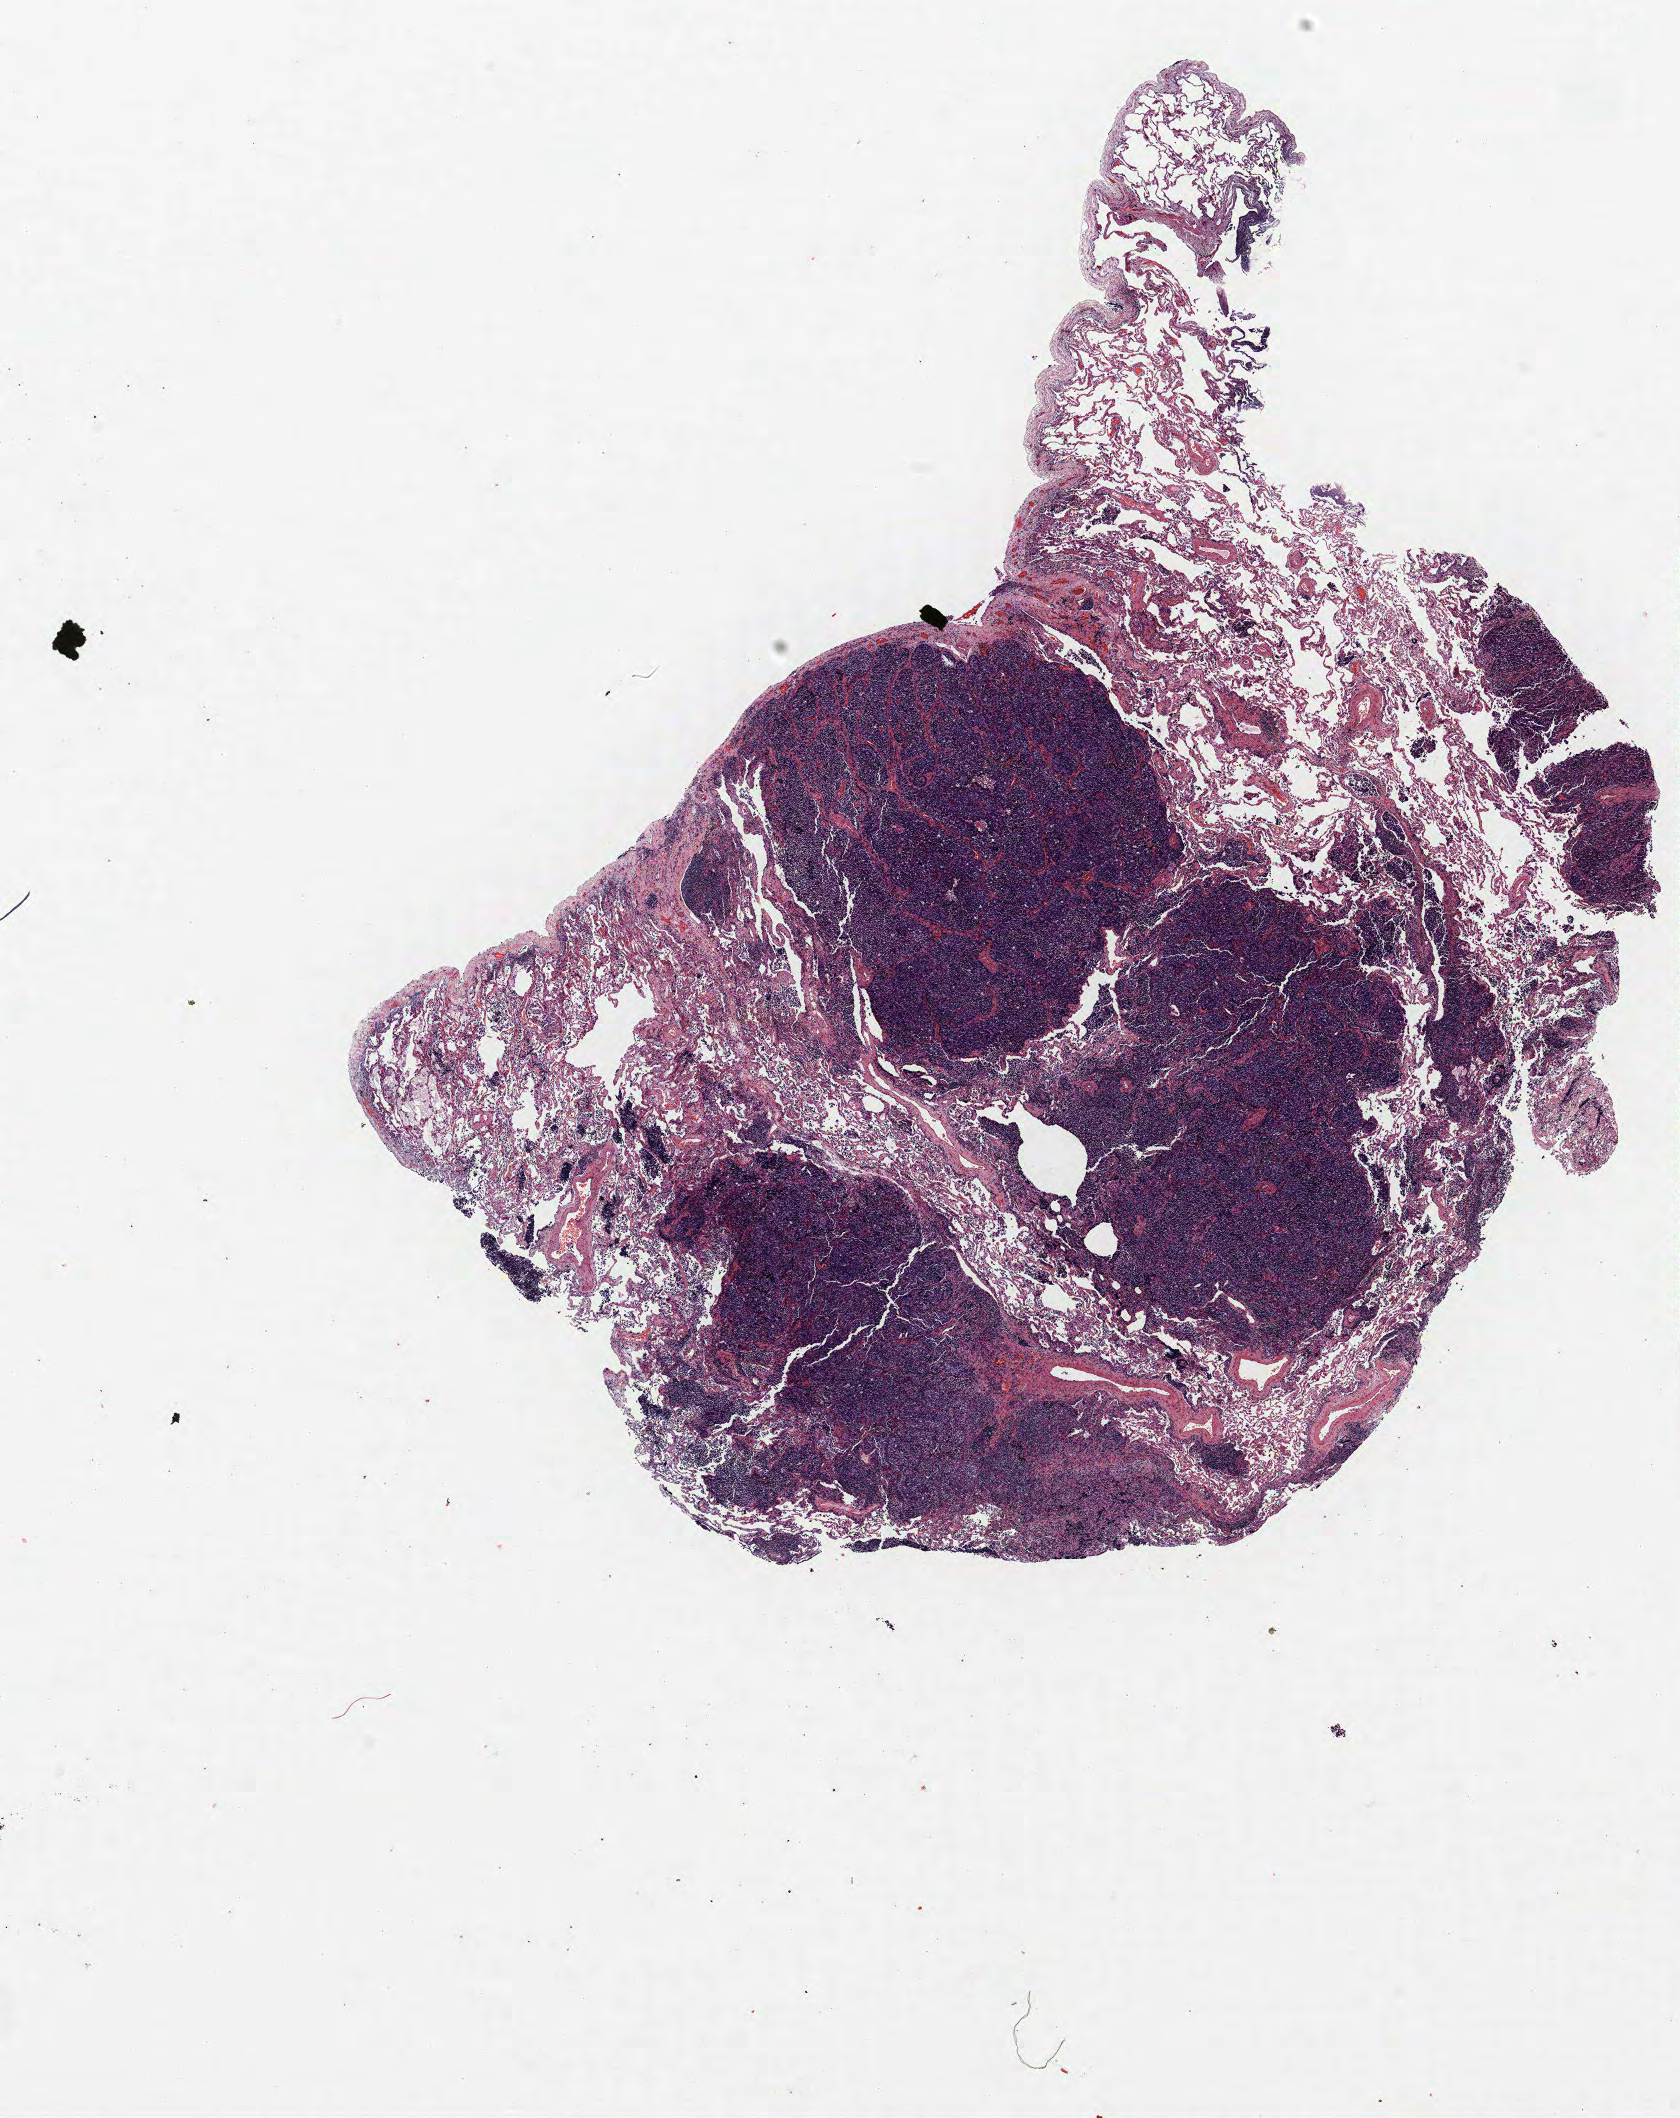
H&E-stained whole-slide image, a low-resolution overview of the entire scanned area, about 13.4 x 16.9 mm (slide scanned at 40x); FFPE section; lung tissue. Male, age 64 at enrolment. Former smoker at enrolment. Grade: poorly differentiated (G3).
Tumour size (pathology): 11 mm. Participant's lung-cancer diagnosis: Adenocarcinoma, NOS. Stage (AJCC 6th edition): IA. Primary tumour location (clinical record): right upper lobe.